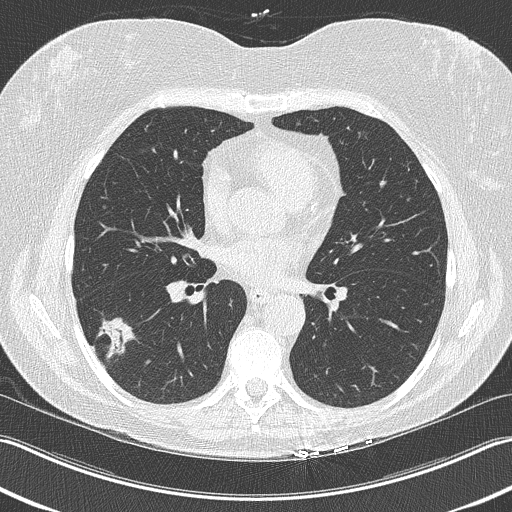
Low-dose screening chest CT, one axial slice; slice 115 of 210 in the series (ordered by position); 120 kVp; lung window (W 1500 / L -600 HU); 512 × 512 image matrix, field of view 348 × 348 mm.
Structures marked on this image (expert manual segmentation):
- lesion 1 (tumor, lower lobe of right lung): bounding box <97,318,137,359> (left, top, right, bottom; pixels)